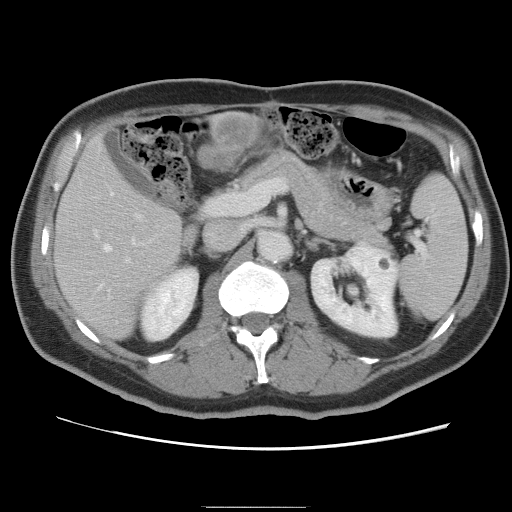
Contrast-enhanced abdominal CT, one axial slice; position 42 of 87 along the scan axis; 120 kVp; intravenous contrast given; soft-tissue window (W 400 / L 40 HU); 5 mm slice thickness; 512 × 512 image matrix, field of view 363 × 363 mm. Male patient, age 63 years. From the clinical record (not read from this slice): diagnosis: colorectal cancer liver metastases, imaged before liver resection; multiple liver metastases: no; largest metastasis: 9 cm; chemotherapy before resection: no.
Annotated regions visible in this slice (expert manual segmentation):
- hepatic veins: bounding box <95,192,135,251> (left, top, right, bottom; pixels)
- liver: <56,114,265,339>
- planned liver remnant (the part of the liver to remain after resection): <55,148,187,340>
- portal vein (with intrahepatic branches): <96,197,144,291>
- liver metastasis: <203,119,256,169>